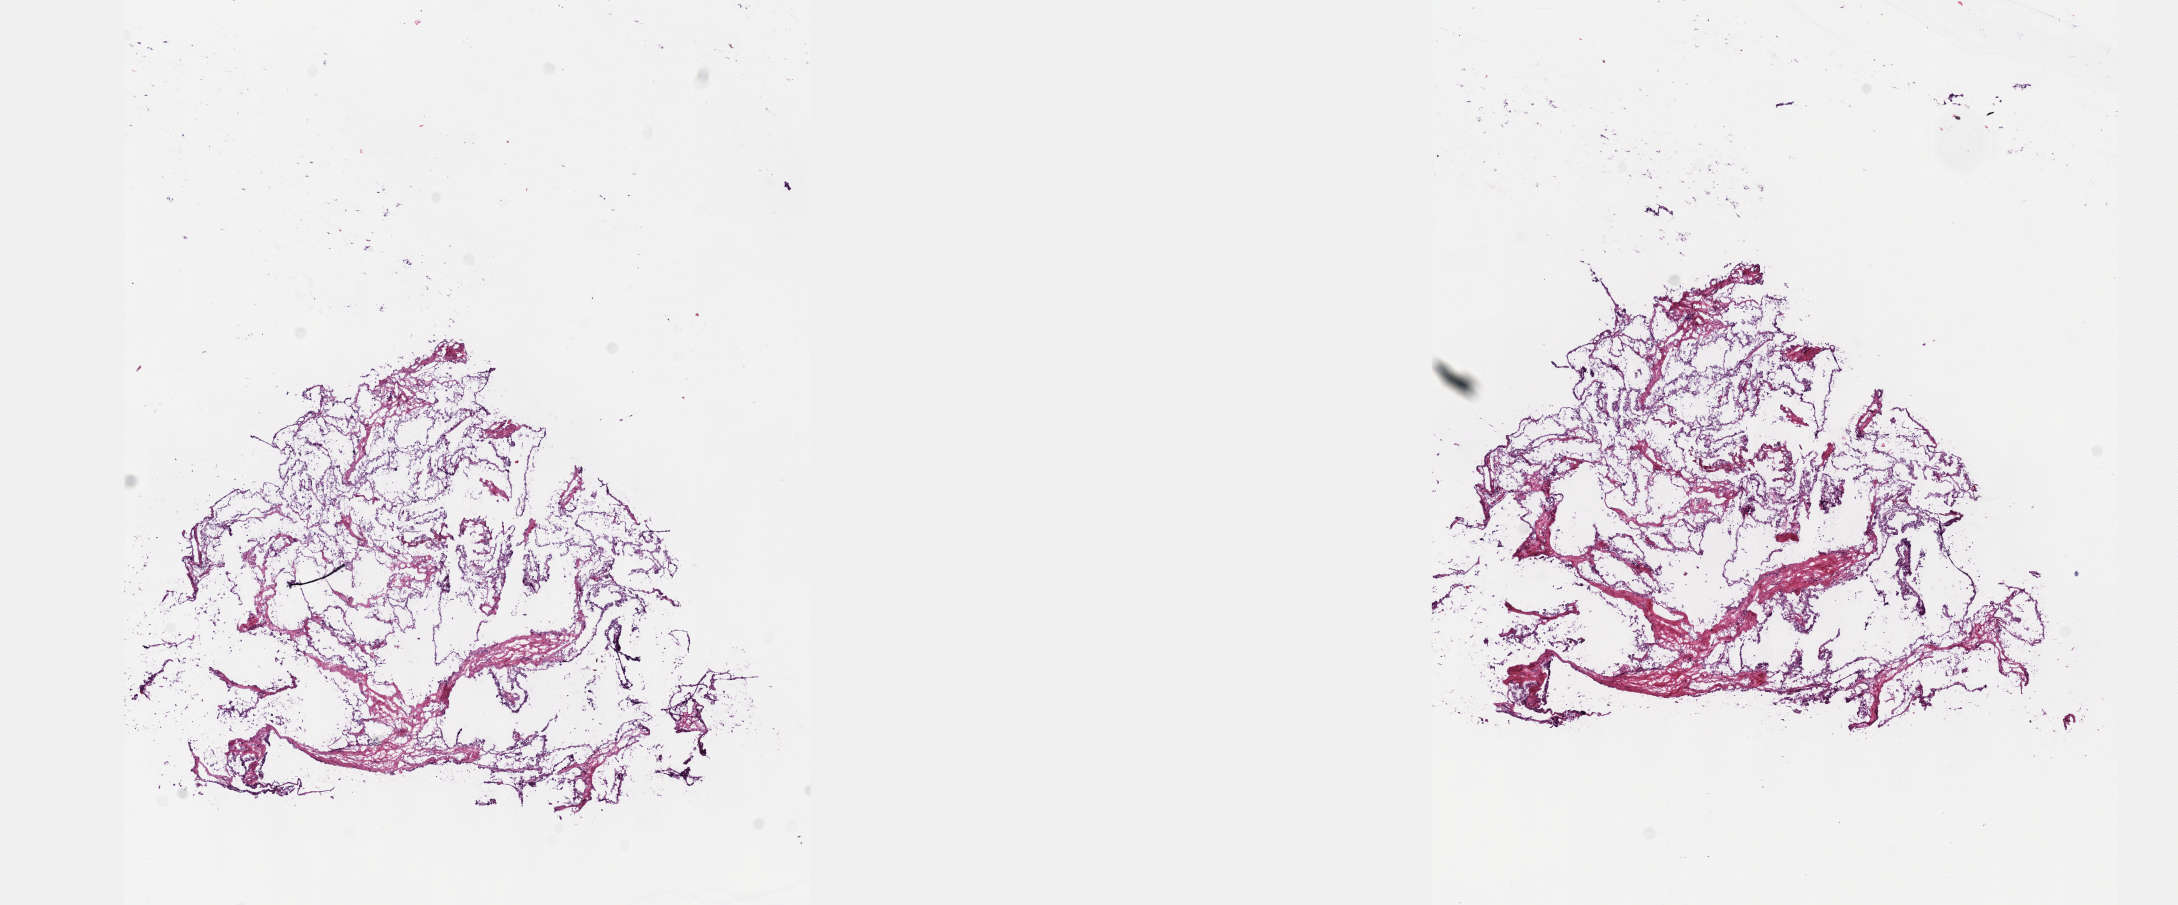
Digitized H&E tissue section (whole slide), a low-resolution overview of the entire scanned area, about 17.6 x 7.3 mm (acquisition: 40x scan); frozen section from the top of the tissue portion; primary tumour sample from the kidney. Patient: female, age at initial diagnosis 68 years. Histologic grade: G2 (moderately differentiated). Pathologist review of this section (percent, as recorded): tumour cells 60%, tumour nuclei 70%, normal cells 0%, stromal cells 30%, necrosis 10%. Infiltration values recorded for this section: lymphocyte infiltration 0%, monocyte infiltration 0%, neutrophil infiltration 0%.
Laterality: right. AJCC pathologic stage: I (7th edition). Pathologic diagnosis: Clear cell adenocarcinoma, NOS.